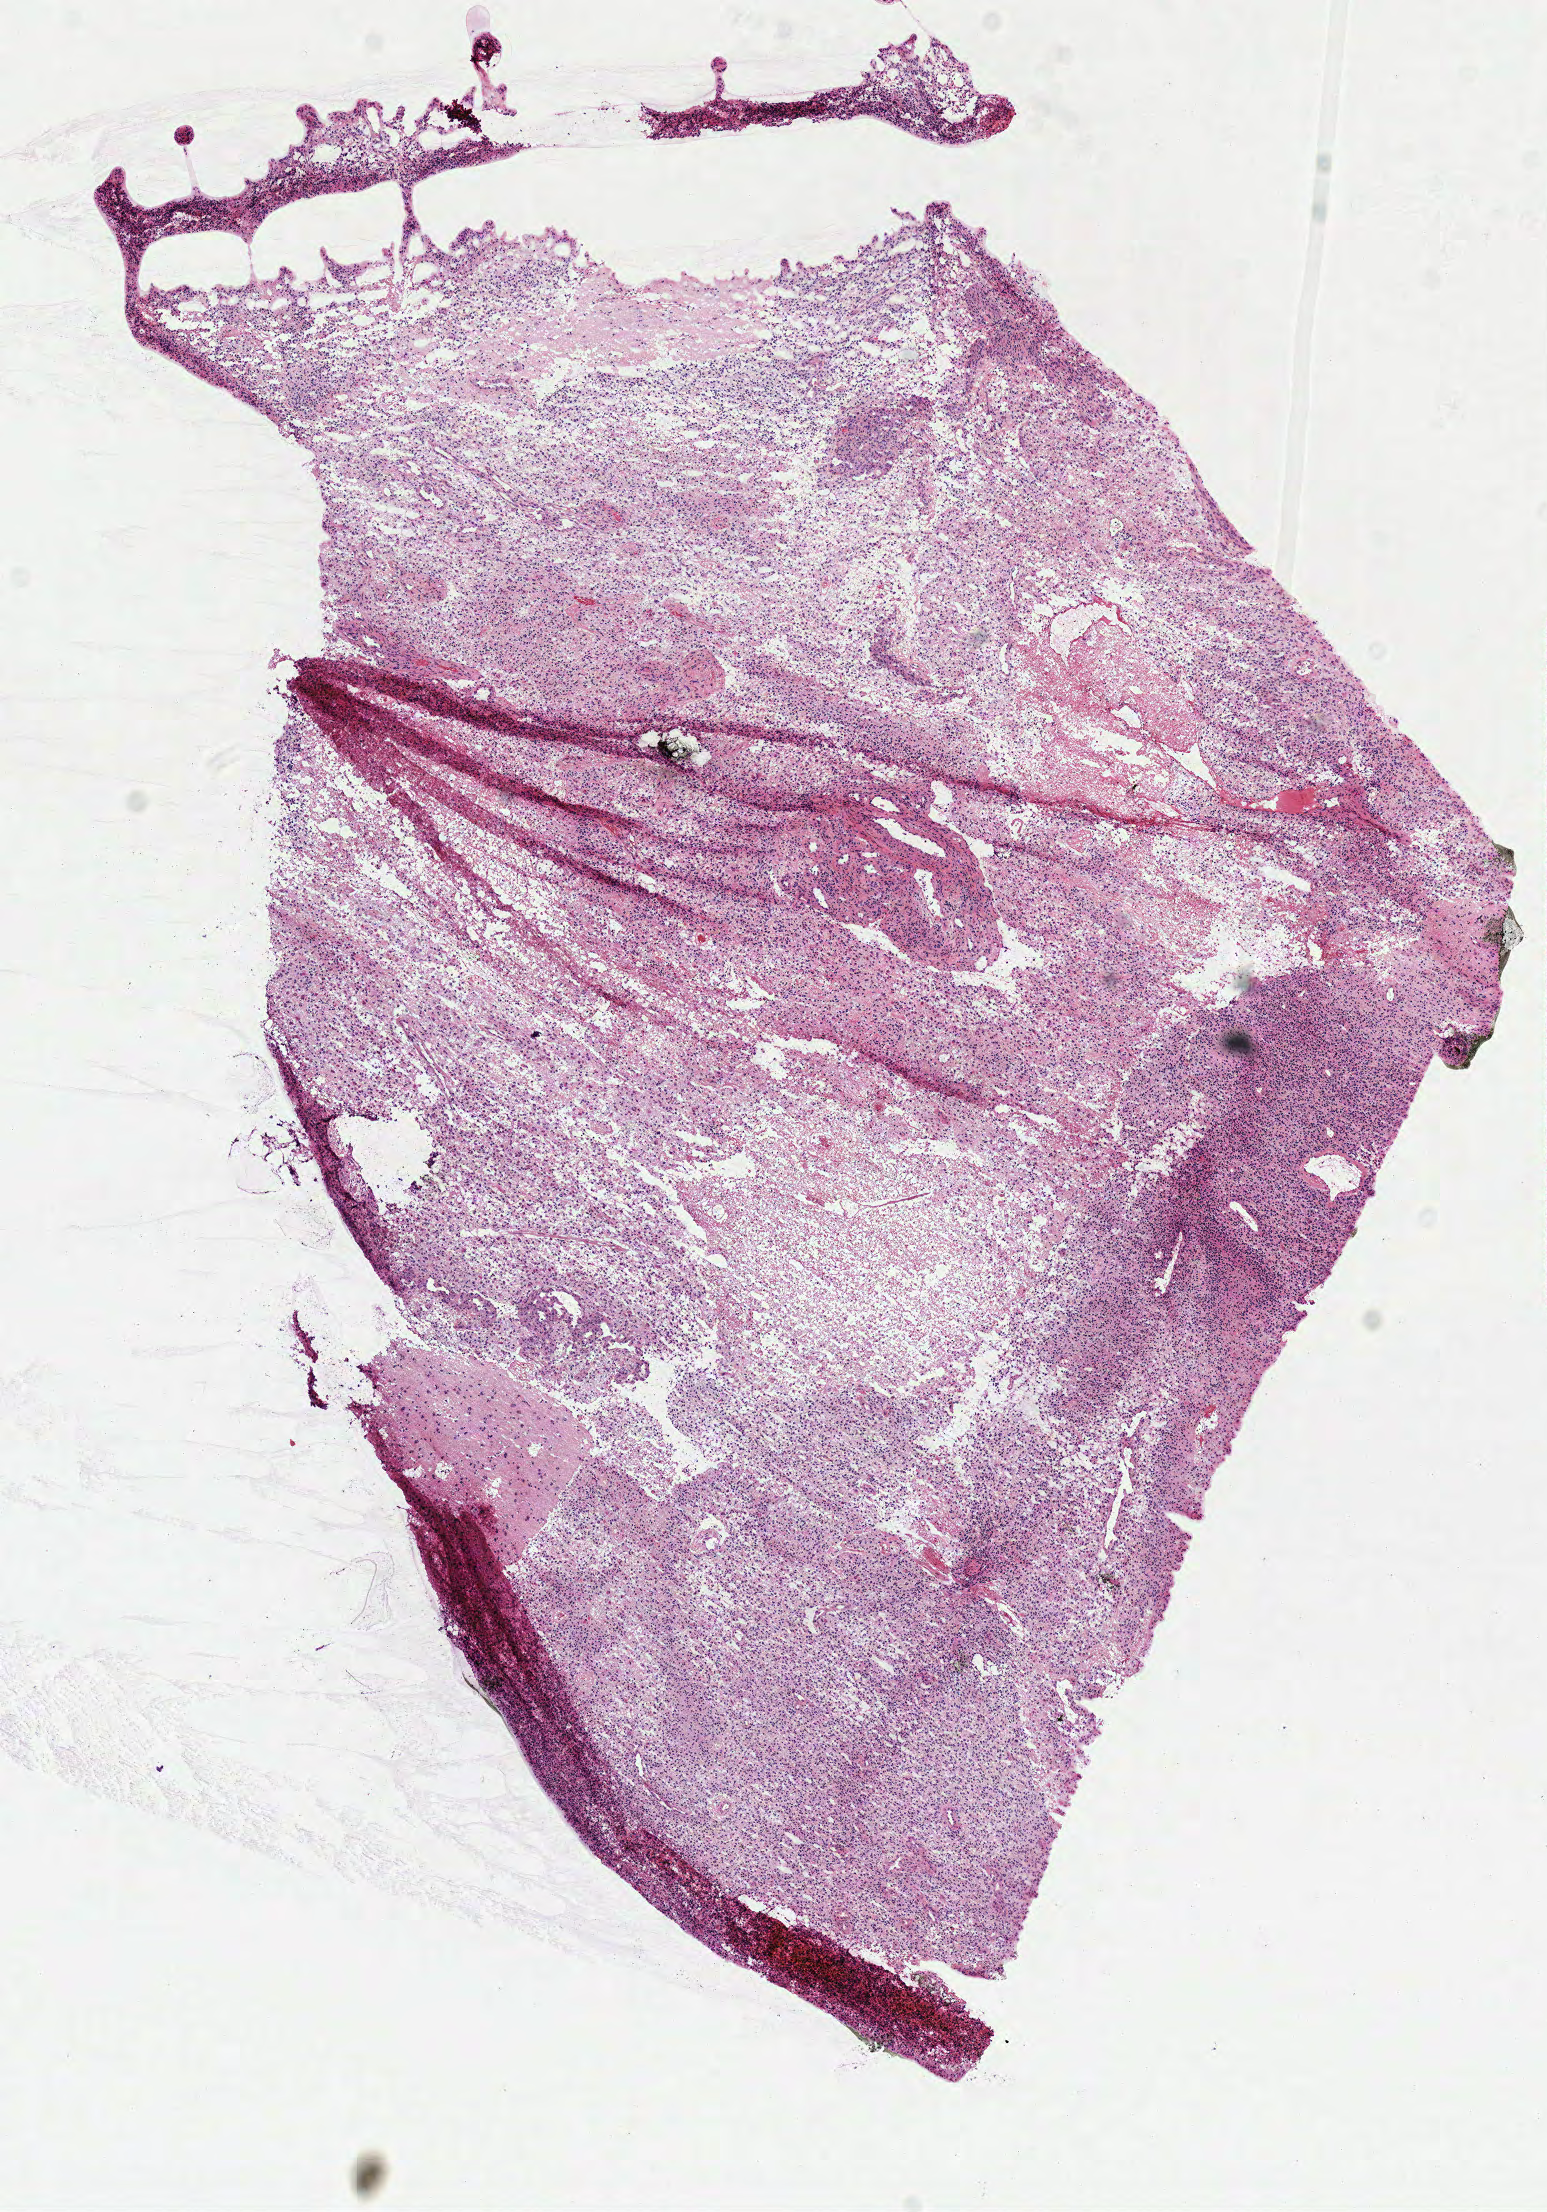
H&E-stained whole-slide image — whole scanned area (about 6.1 x 8.7 mm) shown as a low-resolution overview. Frozen section. Primary tumour sample from the brain. Male patient; age at initial diagnosis 77 years. Pathologist review of this section (percent, as recorded): tumour cells 85%, tumour nuclei 85%, normal cells 0%, stromal cells 0%, necrosis 15%.
Pathologic diagnosis: Glioblastoma.